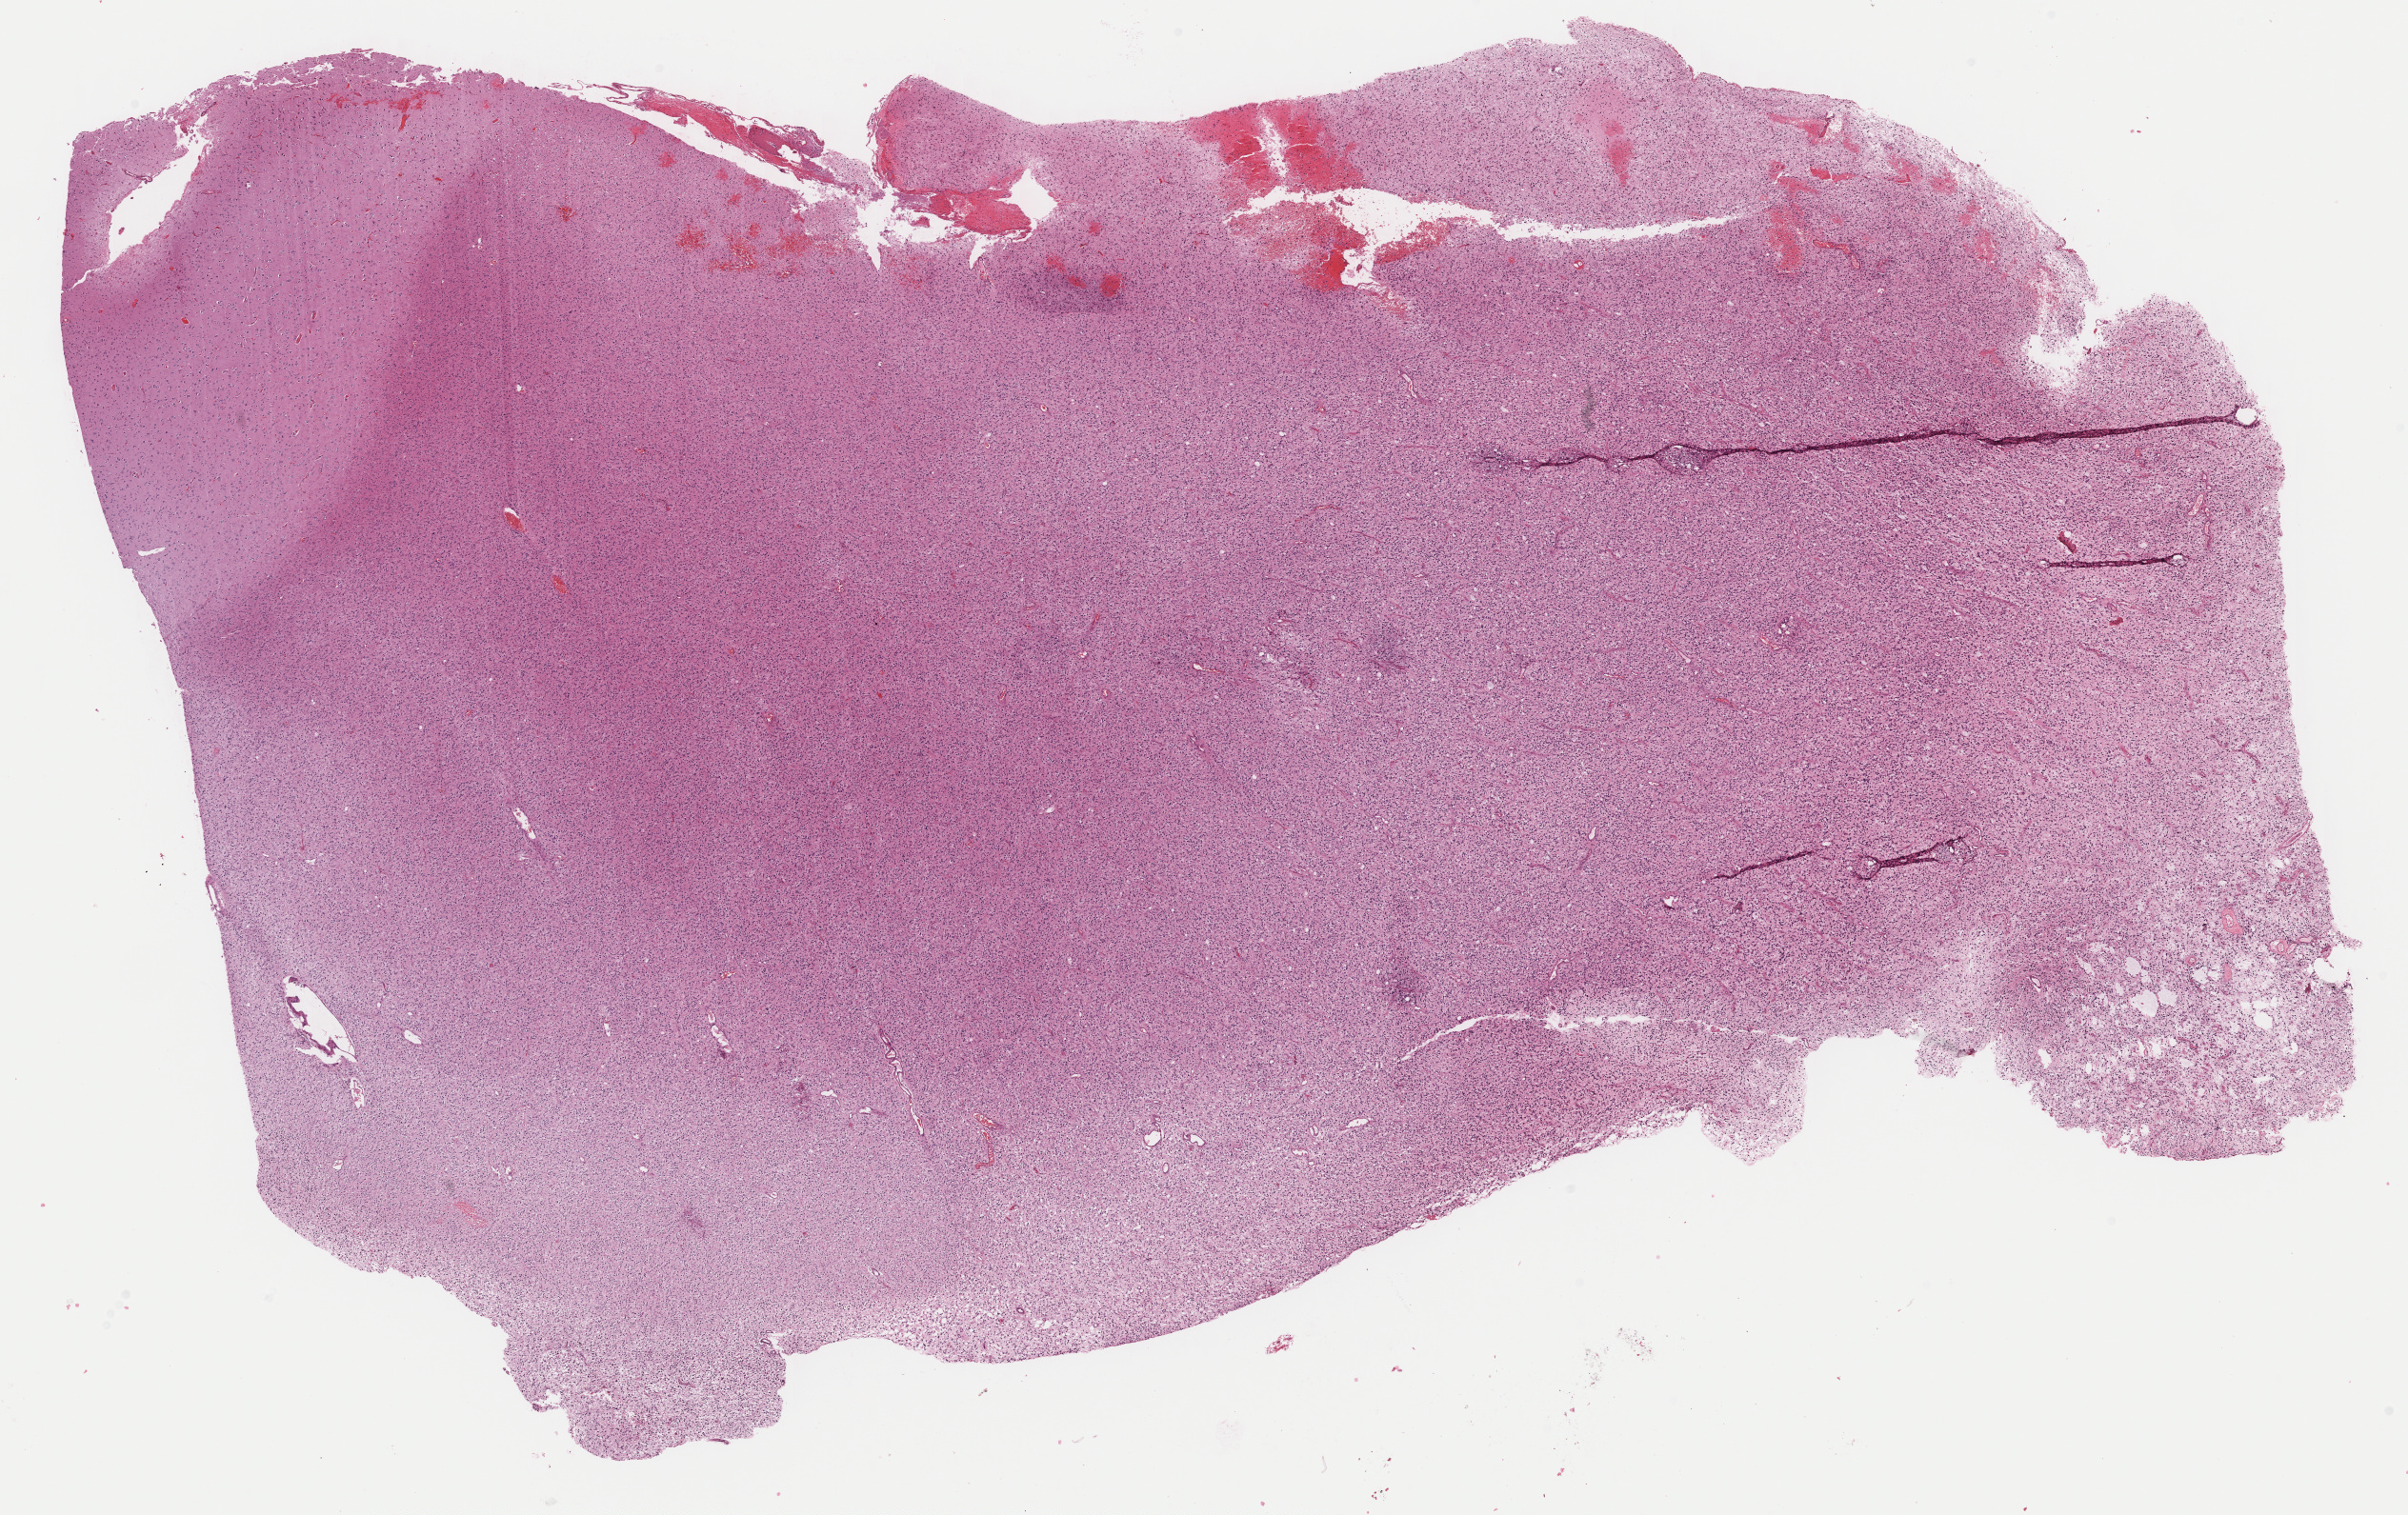
Whole-slide histology image, H&E, whole scanned area (about 19.9 x 12.5 mm, slide scanned at 40x) shown as a low-resolution overview; FFPE section; brain, primary tumour sample. Patient: male, age at initial diagnosis 61 years.
Pathologic diagnosis: Mixed glioma (cerebrum).